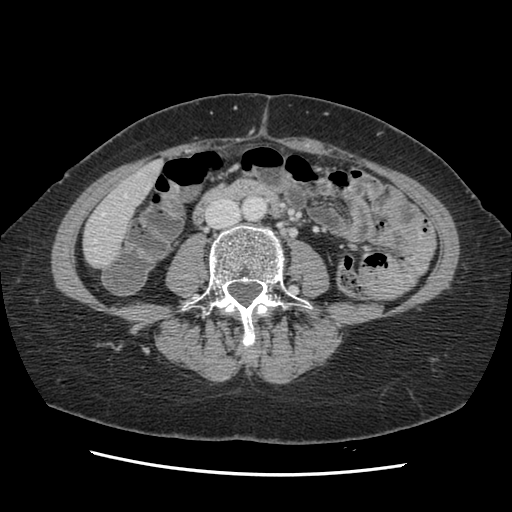
Contrast-enhanced abdominal CT, one axial slice. Position 26 of 141 along the scan axis. Soft-tissue window (W 400 / L 40 HU). 512 × 512 image matrix, field of view 330 × 330 mm. Female patient, age 61 years. Case-level facts recorded for this patient, not image findings: diagnosis: colorectal cancer liver metastases, imaged before liver resection; multiple liver metastases: no; largest metastasis: 2.4 cm; disease in both lobes: no.
Annotated regions visible in this slice (outlined manually by an expert reader):
- hepatic veins: box from (x=93, y=174) to (x=148, y=252) px
- liver: (x=84, y=163)–(x=162, y=267)
- planned liver remnant (the part of the liver to remain after resection): (x=84, y=163)–(x=162, y=267)